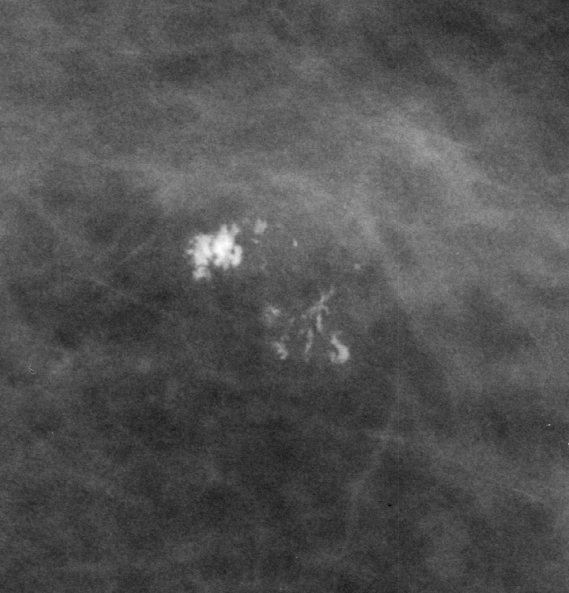
Crop from a digitized film mammogram around one marked abnormality; left breast; CC view.
Finding: calcifications, morphology pleomorphic / fine linear branching, distribution clustered; BI-RADS assessment category 3; pathology (as recorded): benign.